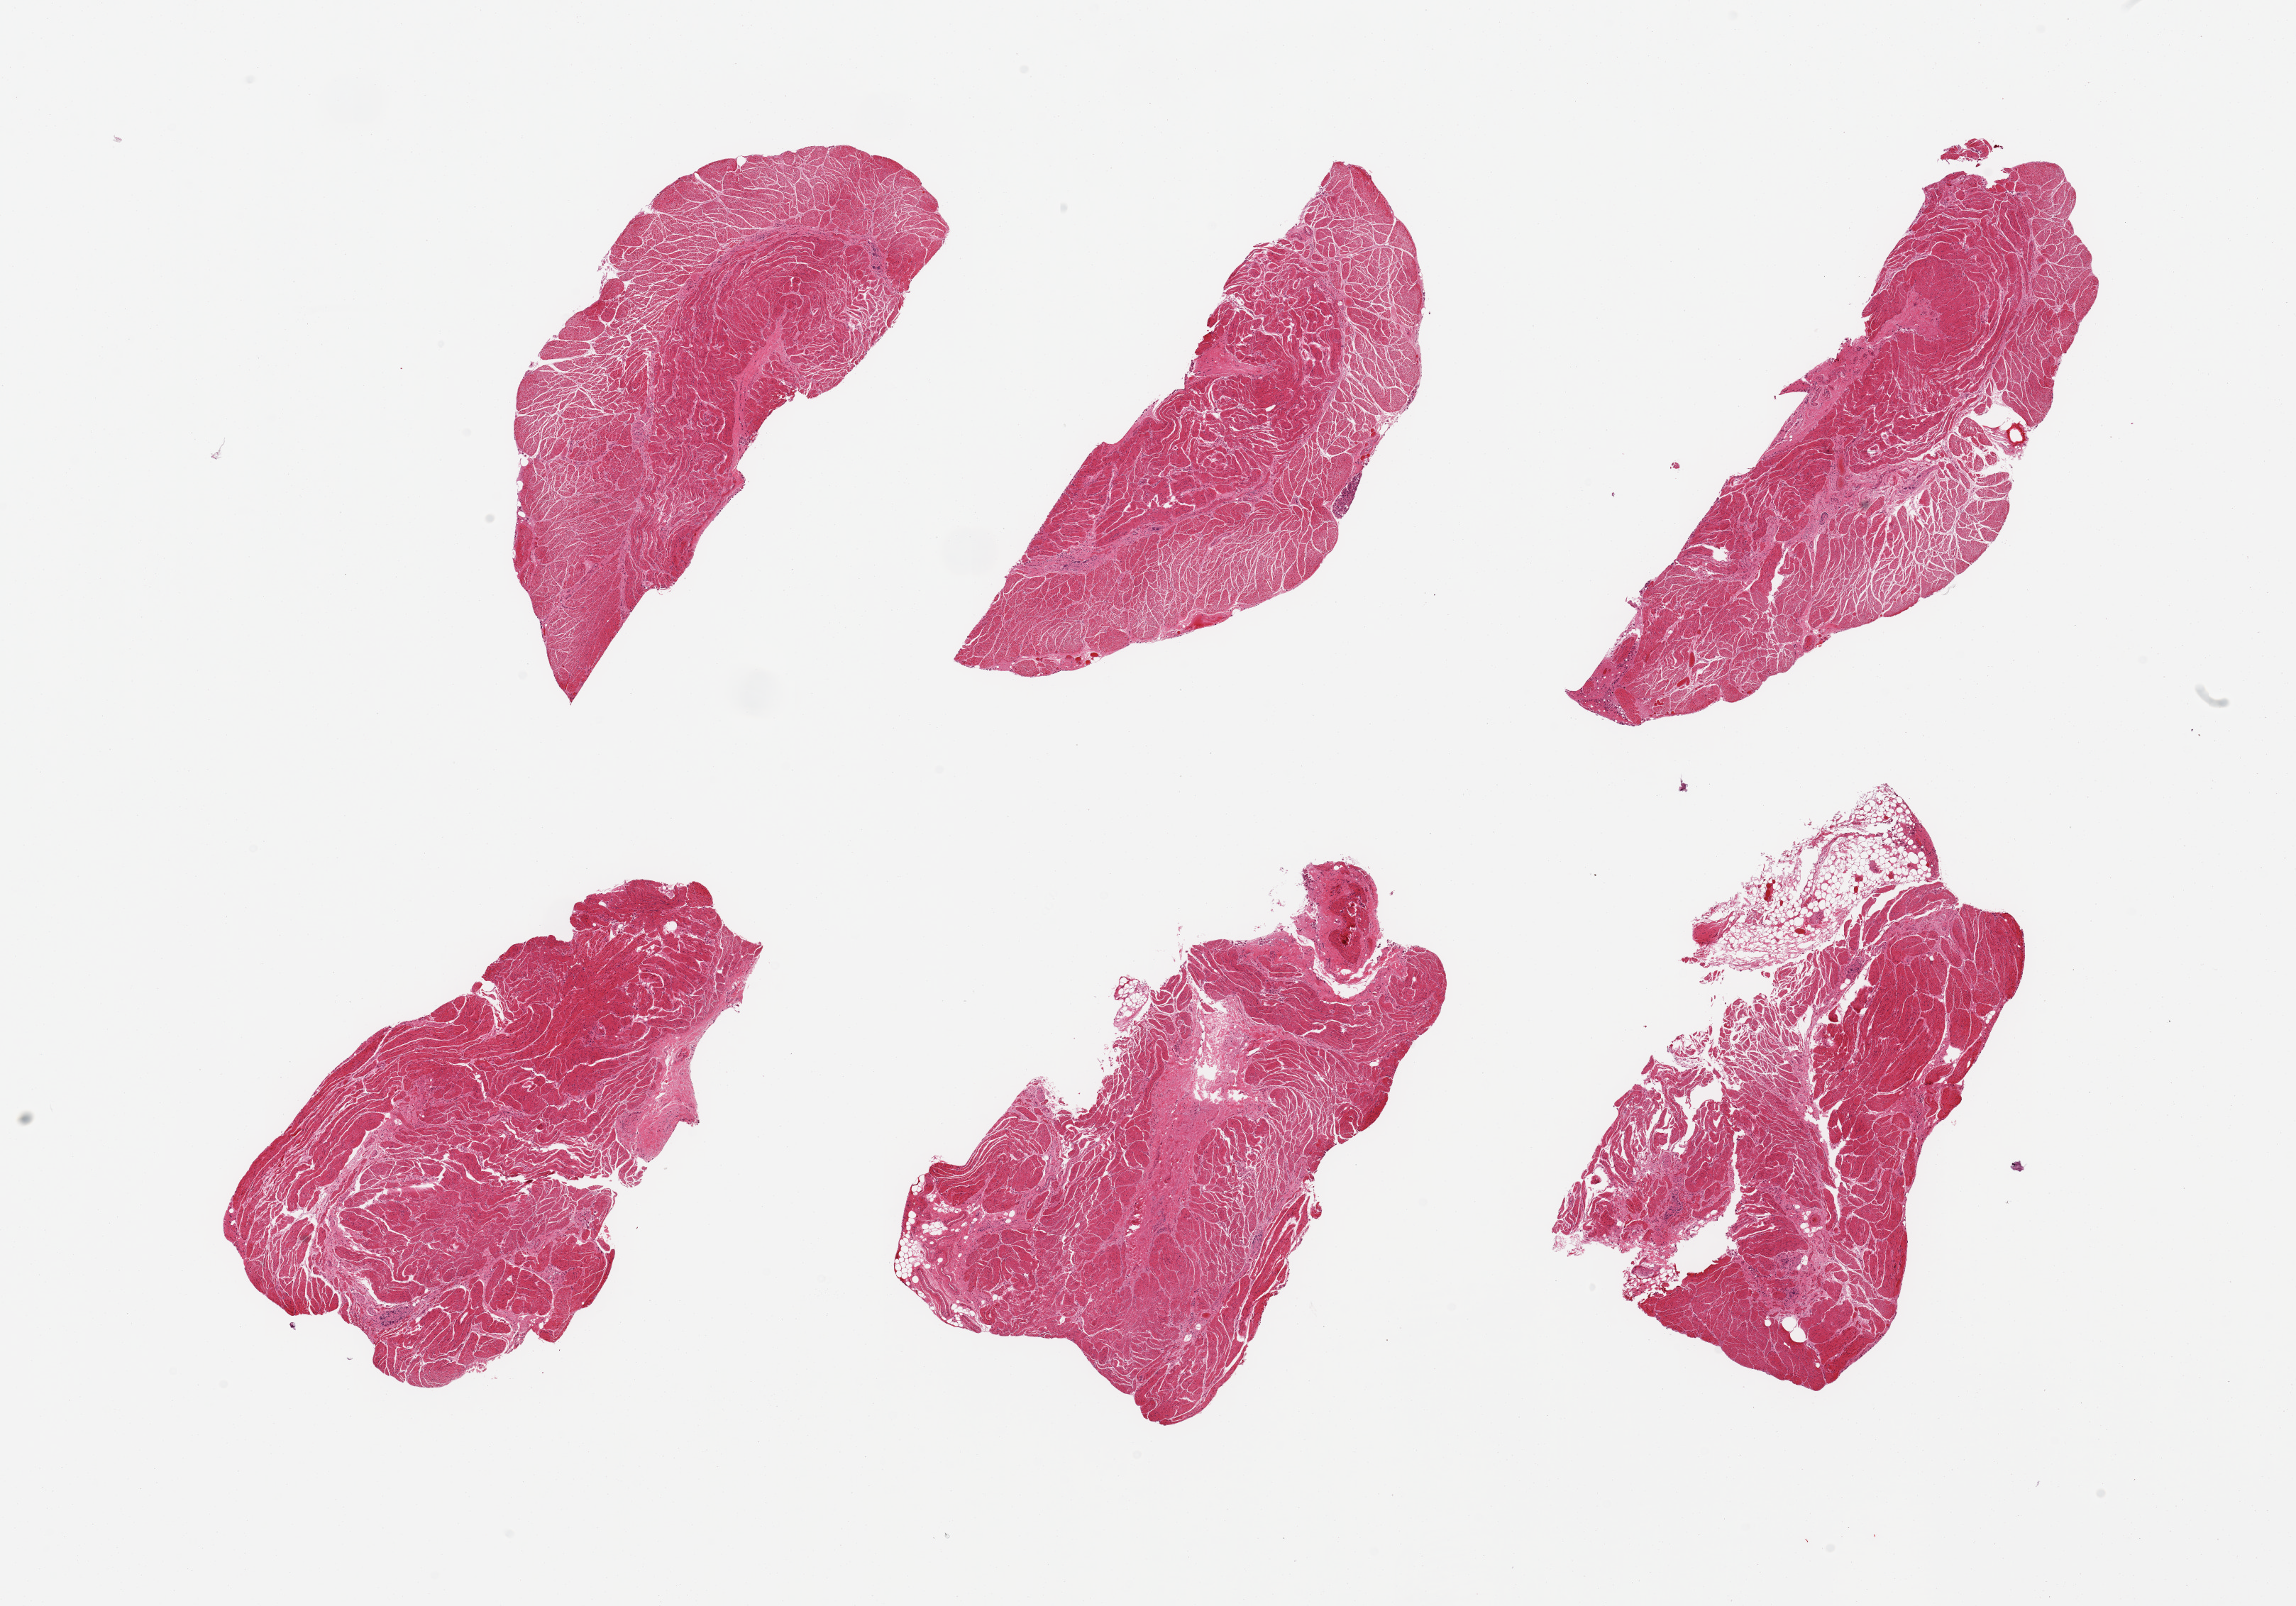
Haematoxylin and eosin whole-slide image, brightfield — low-resolution overview of the scanned area, about 25.6 x 17.9 mm (slide scanned at 20x). PAXgene-fixed, paraffin-embedded tissue. Sampled site (target tissue): esophageal muscle. Donor tissue sample. Donor: male.
- pathologist's review note for this sample: 6 pieces; 1 piece has 25% submucosal fat; well preserved ganglion cells